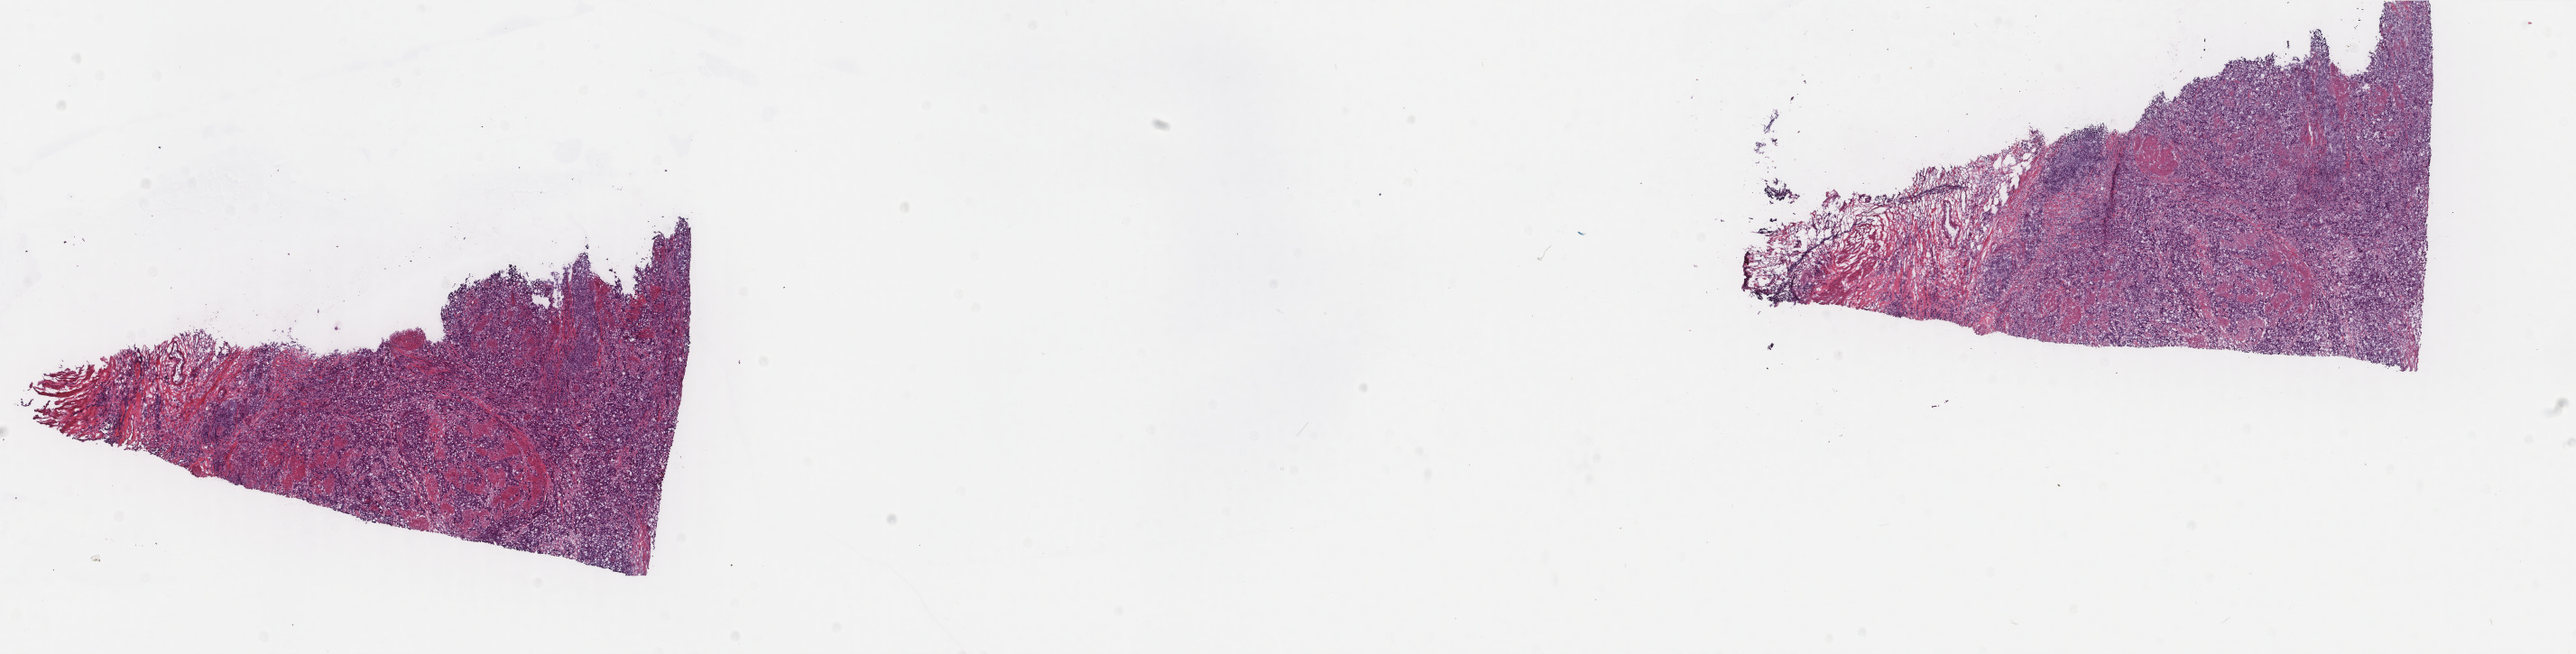
H&E whole-slide image, a low-resolution overview of the entire scanned area, about 22.7 x 5.8 mm (slide scanned at 40x), frozen section, sample: primary tumour, bladder. Female patient; age at initial diagnosis 67 years. Histologic grade: high grade. Pathologist review of this section (percent, as recorded): tumour cells 65%, tumour nuclei 80%, normal cells 0%, stromal cells 35%, necrosis 0%. Infiltration values recorded for this section: lymphocyte infiltration 3%, monocyte infiltration 0%, neutrophil infiltration 0%.
* lymph nodes positive (case pathology): 0 of 29 examined
* TNM: T3 N0 M0
* AJCC pathologic stage: III
* pathologic diagnosis: Transitional cell carcinoma (dome of bladder)